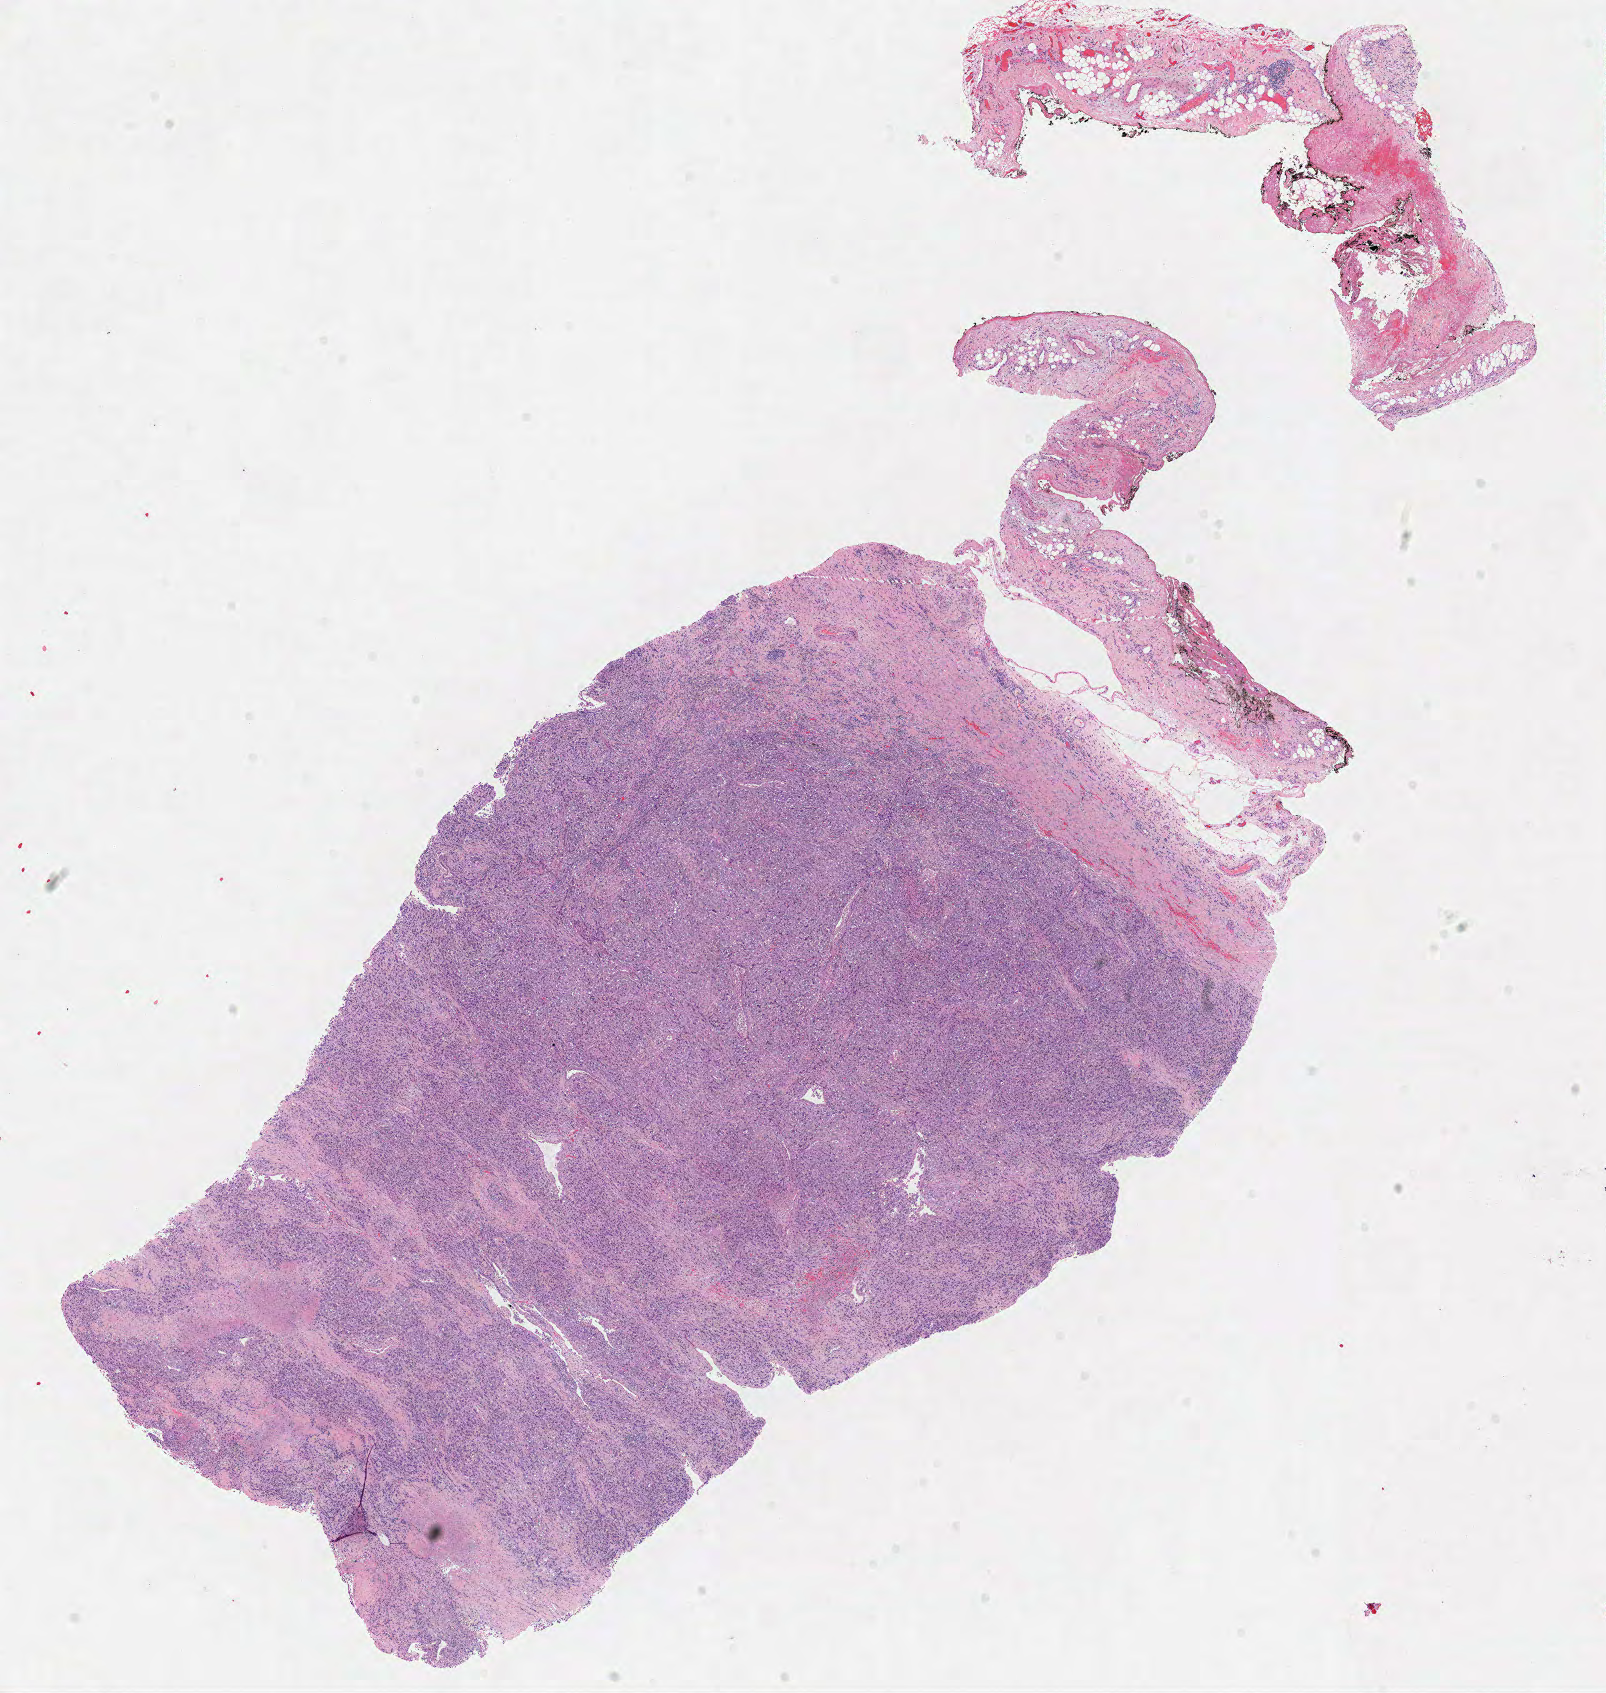
Digitized H&E tissue section (whole slide), low-resolution overview of the scanned area, about 12.7 x 13.3 mm (from a 40x scan). Frozen section from the top of the tissue portion. Sample: primary tumour, lung. Male patient; age at initial diagnosis 59 years. Composition of this section per pathologist review: tumour cells 85%, tumour nuclei 80%.
Histologic diagnosis: Adenocarcinoma, NOS (upper lobe, lung).